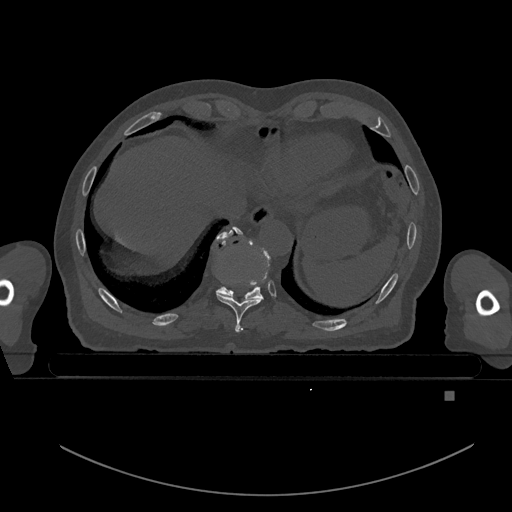
CT including the spine, one axial slice. Position 124 of 969 along the scan axis. Bone window (W 1800 / L 400 HU). 0.5 mm slice thickness. 512 × 512 image matrix, field of view 456 × 456 mm. Male patient, age 82 years. From the clinical record (not read from this slice): primary cancer: prostate.
Structures marked on this image (semi-automatically segmented with operator editing):
- T10 vertebra: box from (x=218, y=226) to (x=269, y=298) px
- T9 vertebra: (x=215, y=230)–(x=263, y=332)